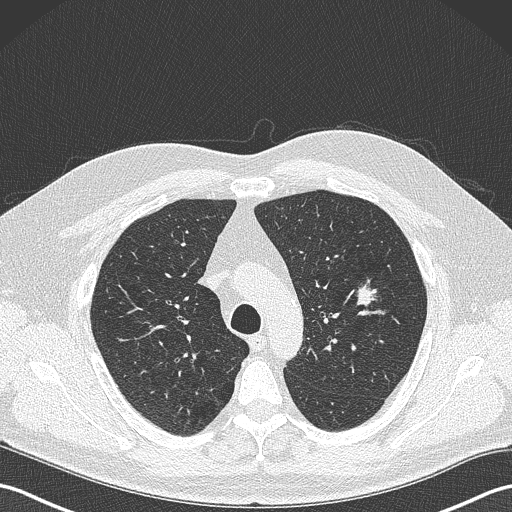
Low-dose screening chest CT, one axial slice; position 252 of 343 along the scan axis; reconstruction kernel B50f; lung window (W 1500 / L -600 HU); 512 × 512 image matrix, field of view 350 × 350 mm.
Outlined on this slice (manually delineated by an expert):
- lesion 1 (tumor, upper lobe of left lung): box from (x=357, y=284) to (x=377, y=306) px